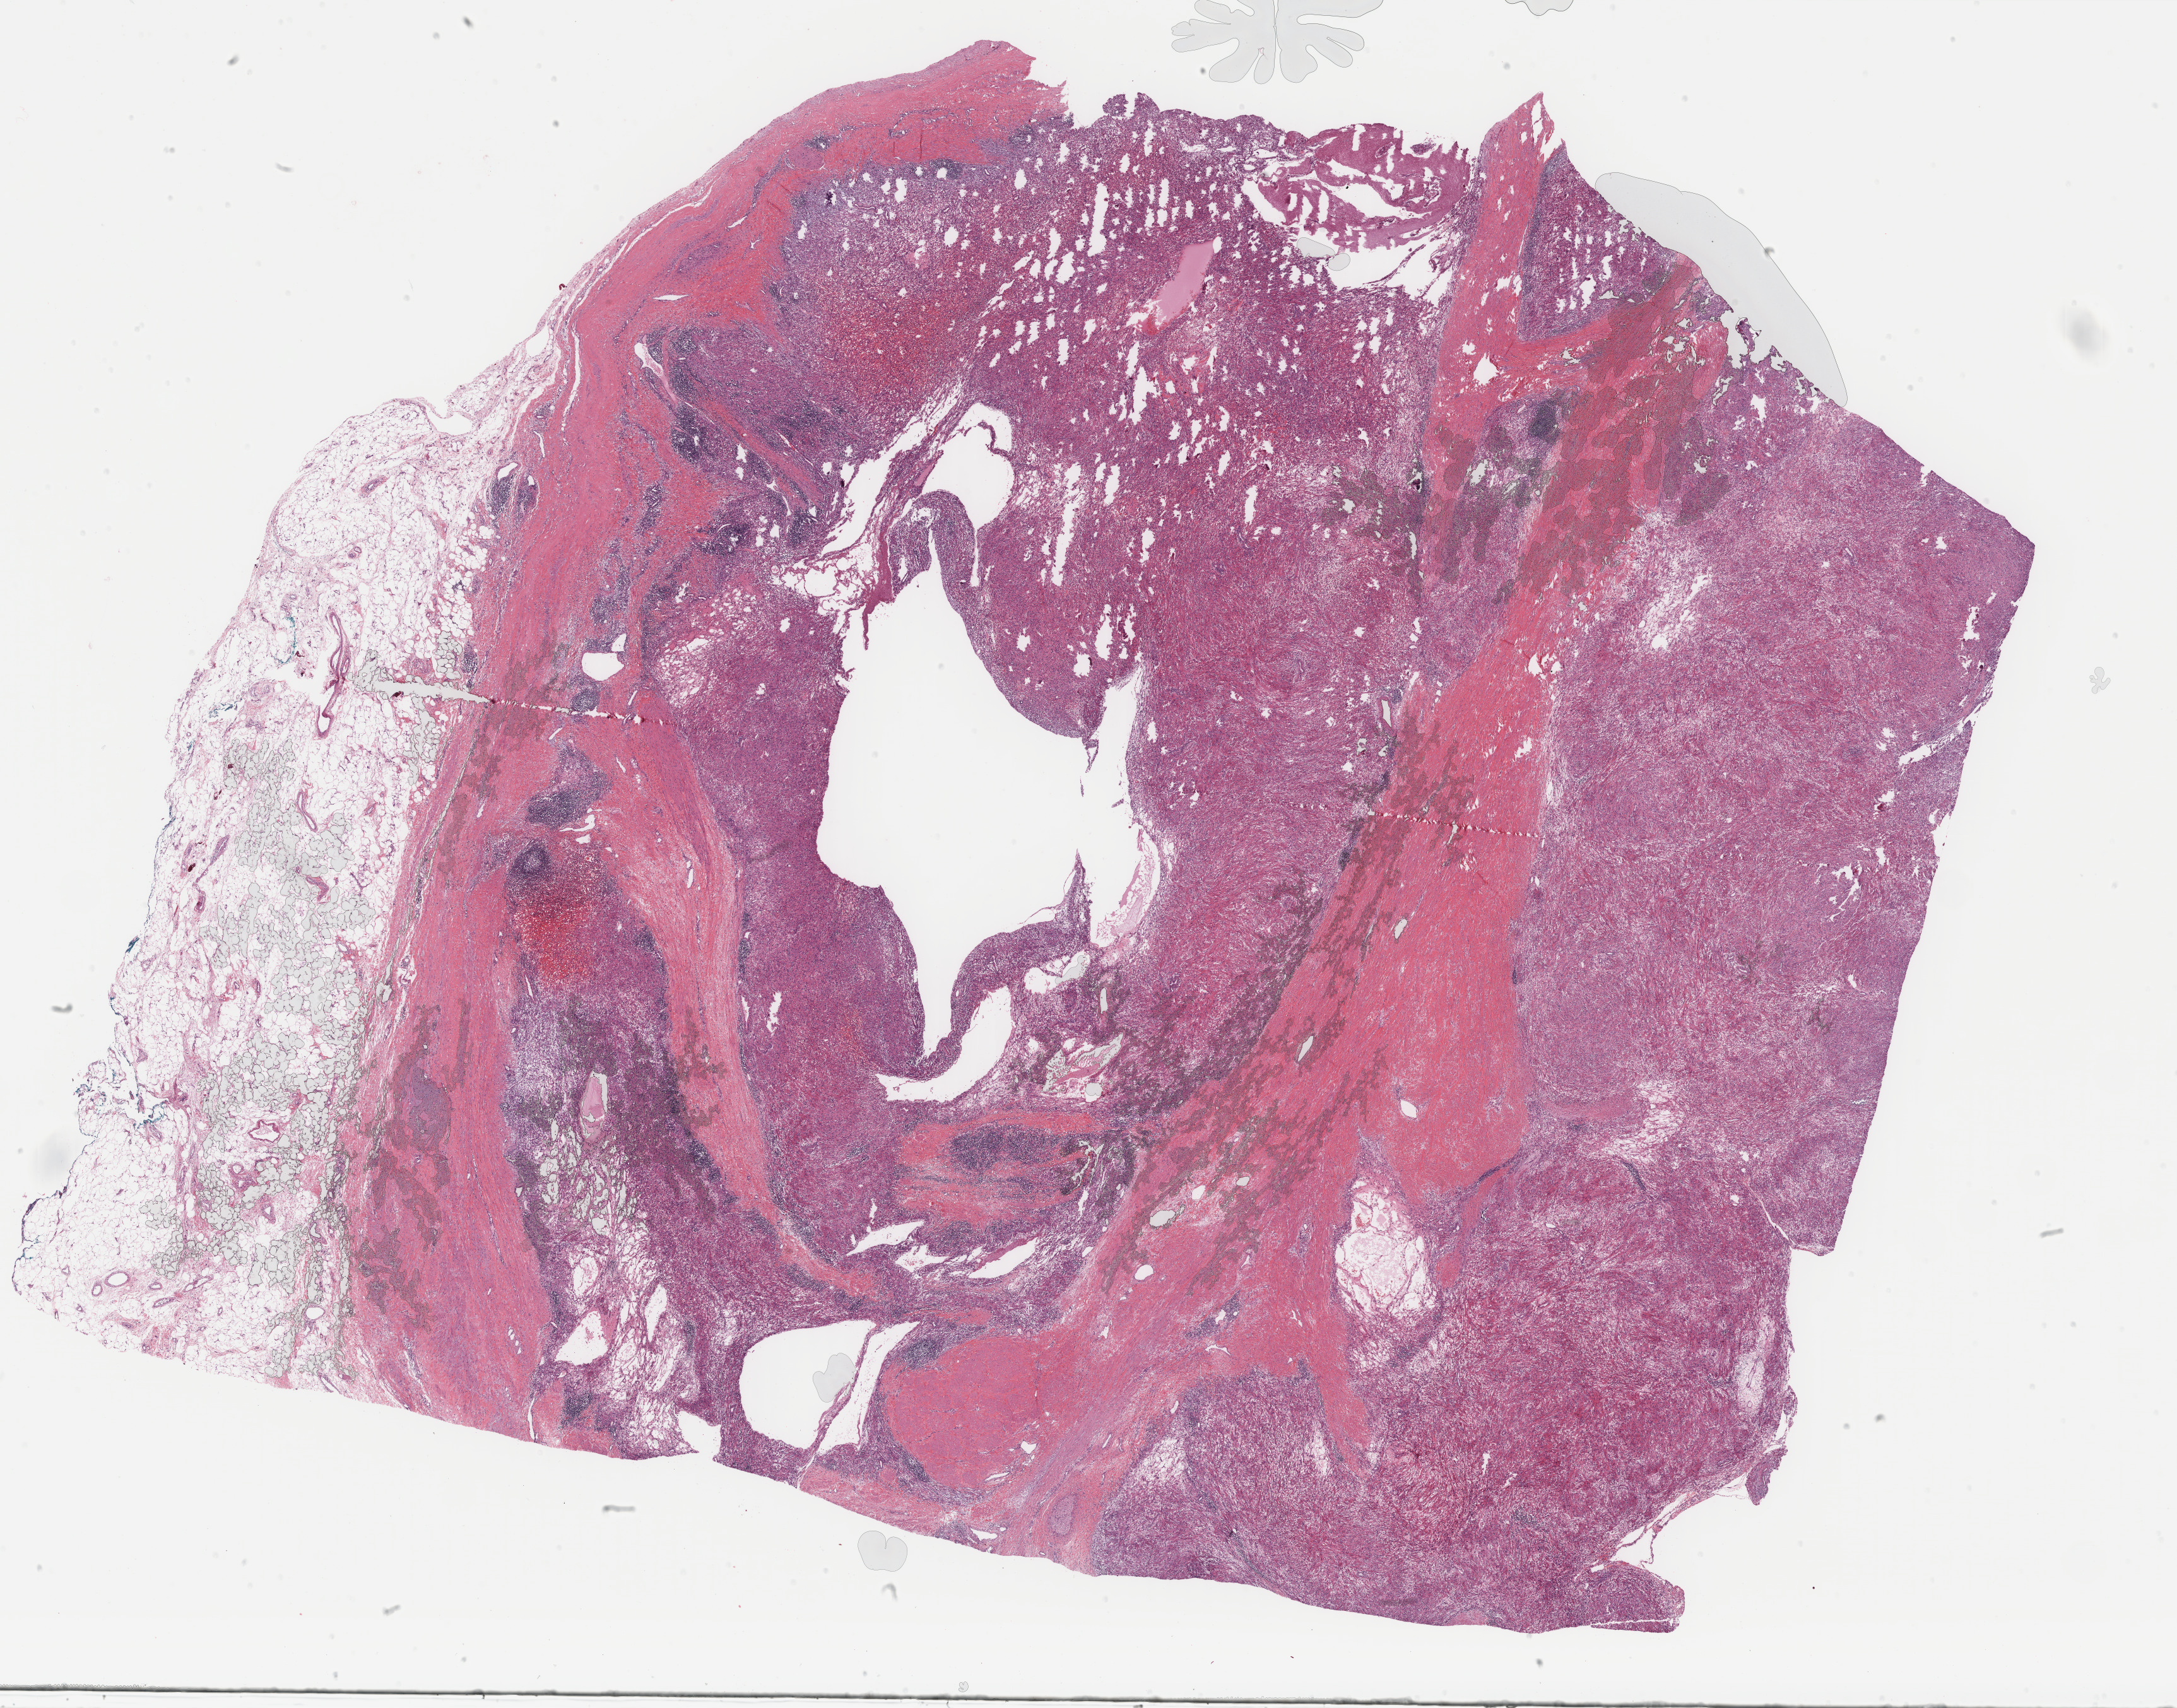
H&E-stained whole-slide image, low-resolution overview of the scanned area, about 27.4 x 21.5 mm (slide scanned at 40x). Formalin-fixed paraffin-embedded (FFPE) diagnostic section. Primary tumour sample from the connective, subcutaneous and other soft tissues. Patient: male, age at initial diagnosis 42 years.
Diagnosis: Leiomyosarcoma, NOS (connective, subcutaneous and other soft tissues of pelvis).